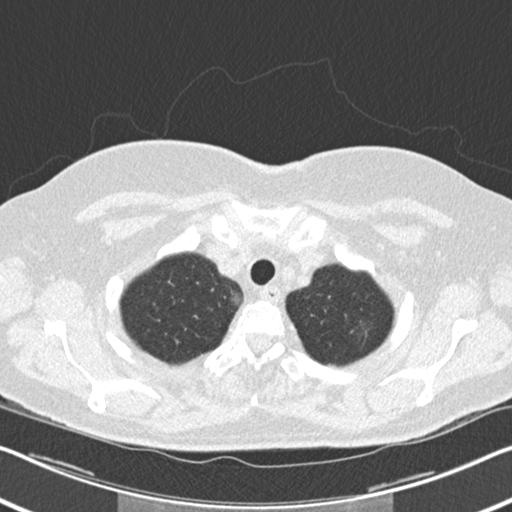
Chest CT (low-dose screening protocol), one axial image, second screening round (one year after baseline), lung window (W 1500 / L -600 HU), slice 30 of 202 in the series. Female, age 60 years at enrolment. Current smoker at enrolment.
Expert-annotated lung lesion, box from (x=337, y=311) to (x=380, y=351) px. The screening reader recorded 6 non-calcified nodules or masses ≥4 mm on this exam (right upper lobe, right middle lobe, right lower lobe, right lower lobe, left lower lobe, lingula); which of them this box marks is not recorded. Official screen result: positive, change unspecified: nodule(s) >= 4 mm or enlarging nodule(s), mass(es), or other non-specific abnormalities suspicious for lung cancer. Participant outcome: lung cancer diagnosed 495 days after this screen — non-small cell carcinoma, left upper lobe, poorly differentiated (G3), stage IB (AJCC 6th edition), 7 mm at pathology.